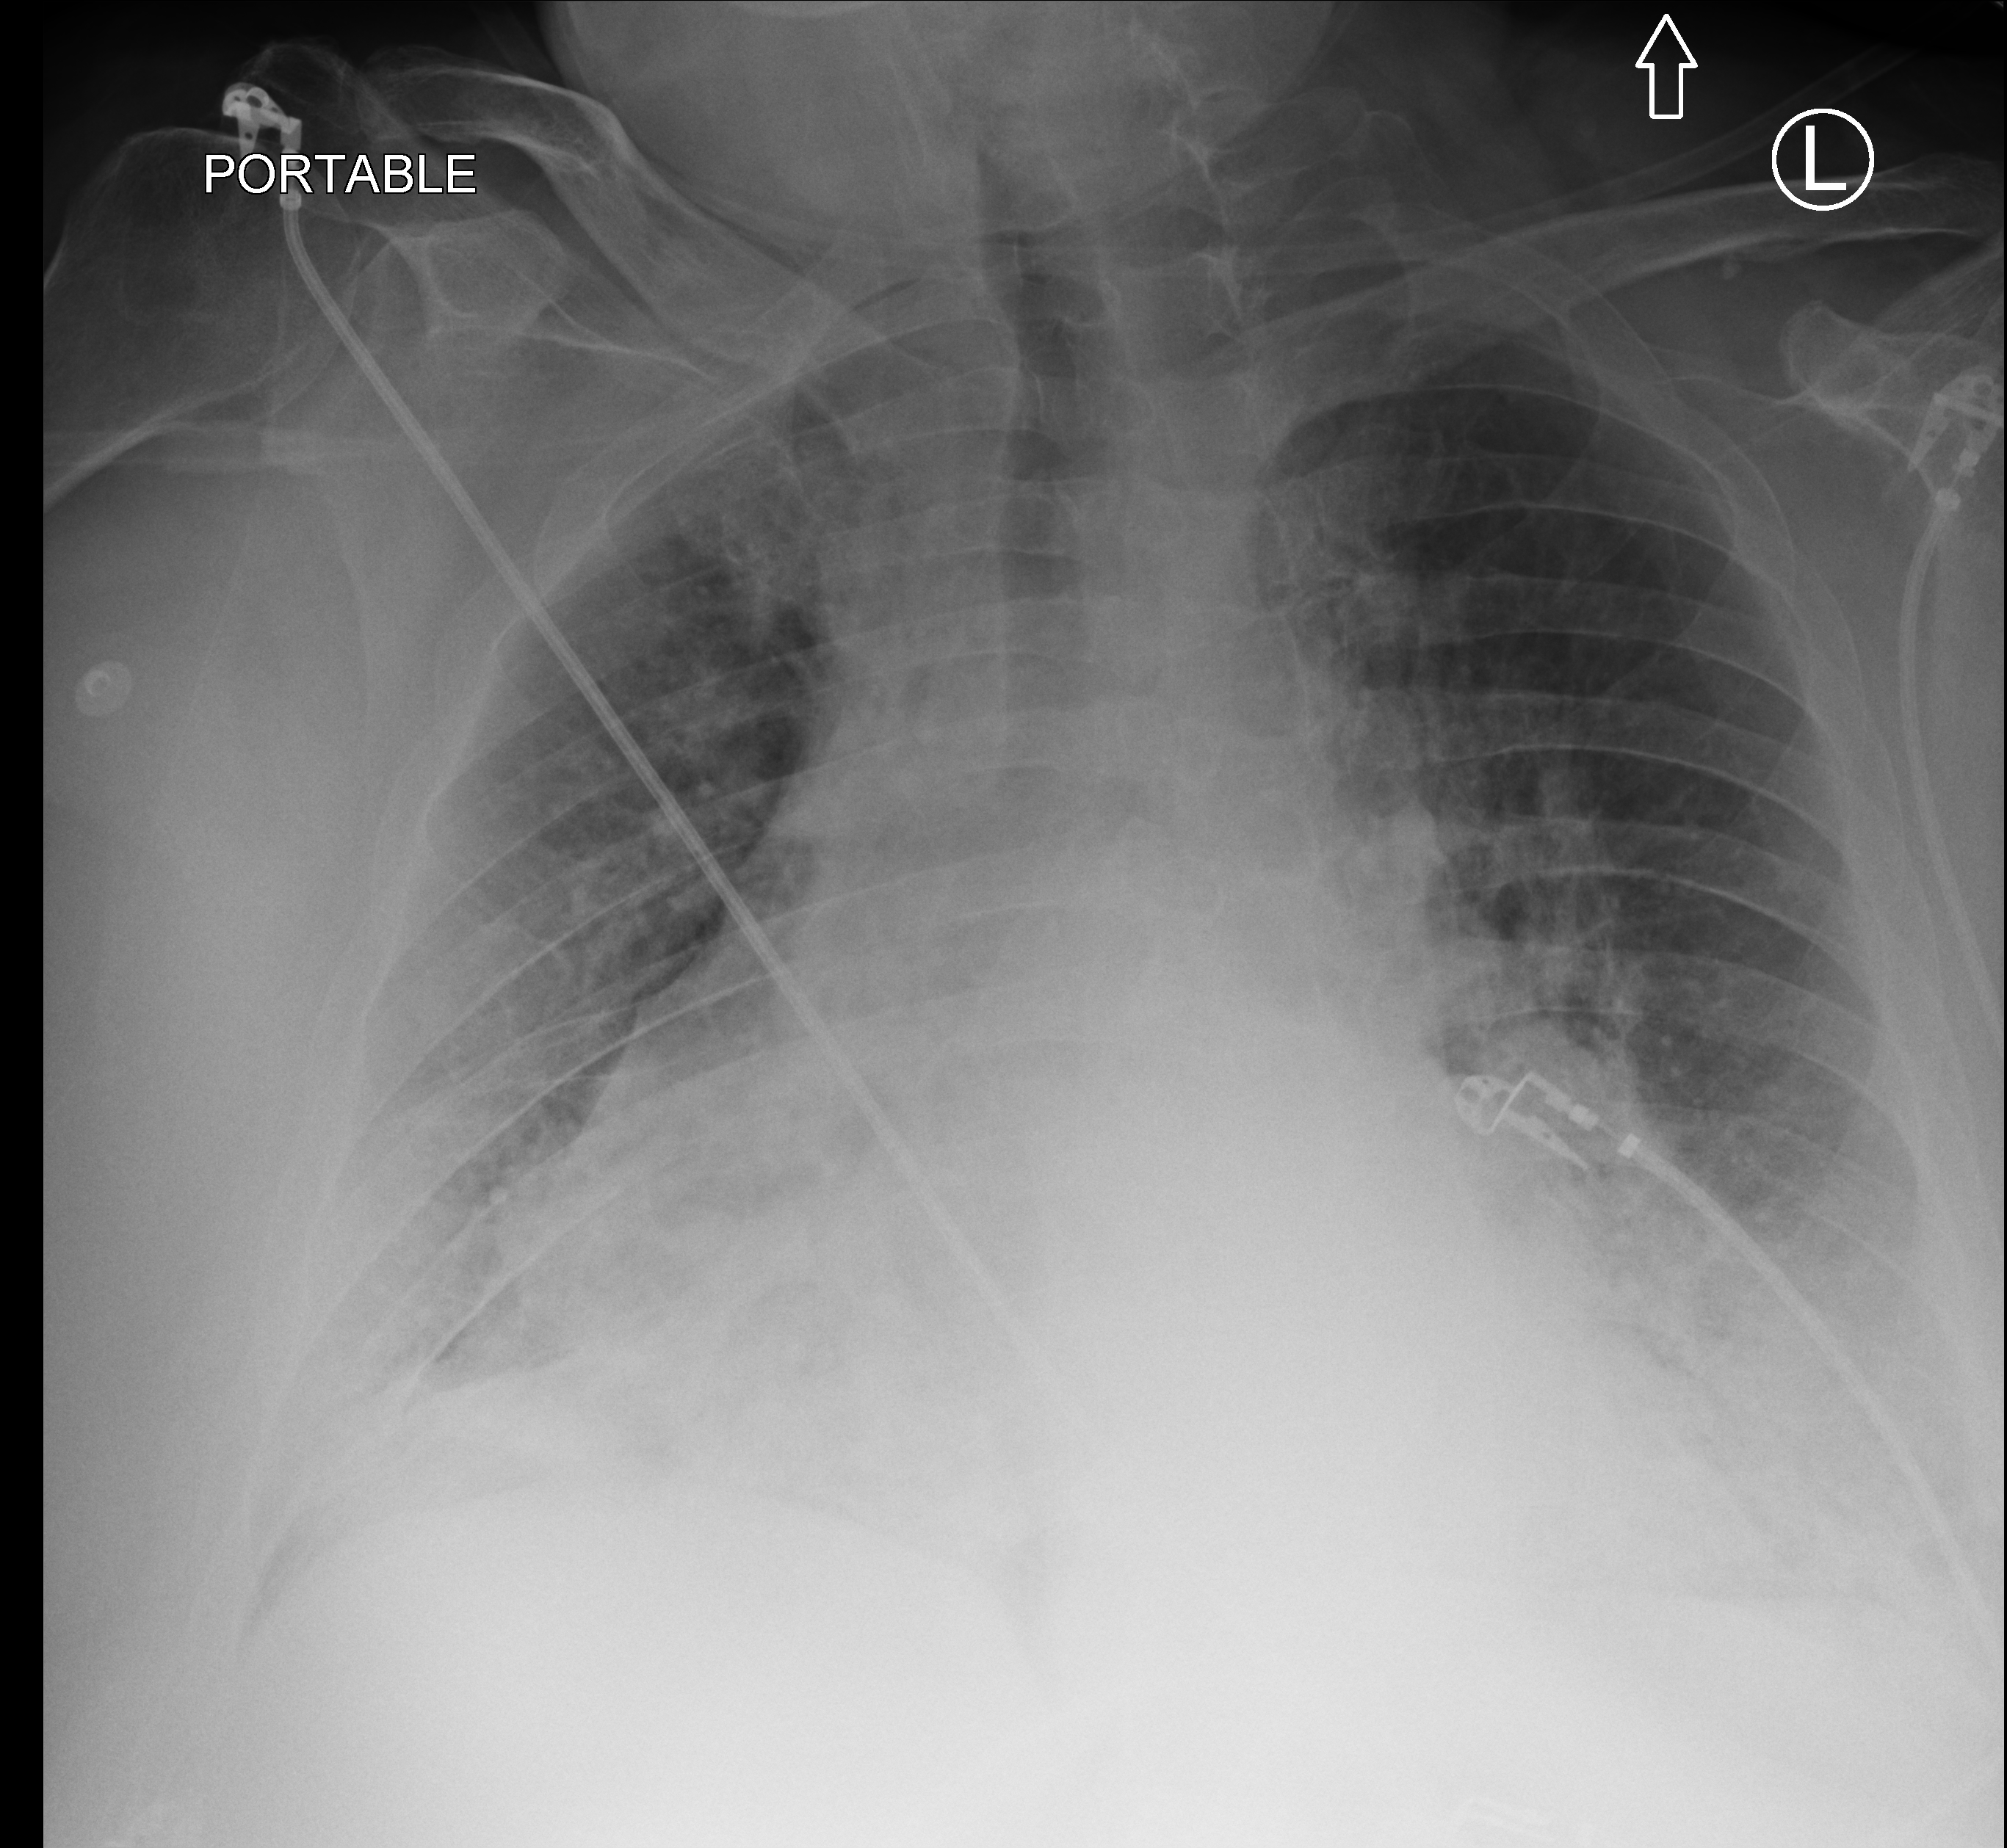
Bedside chest radiograph (computed radiography), anteroposterior (AP) projection. Patient hospitalised with COVID-19; male, aged 60–74 years.
From the hospital-stay record, not from the radiograph (when in the stay this image was taken is not recorded): mechanically ventilated during this hospital stay: yes; COPD (admission record): no; admitted to intensive care during this hospital stay: yes.